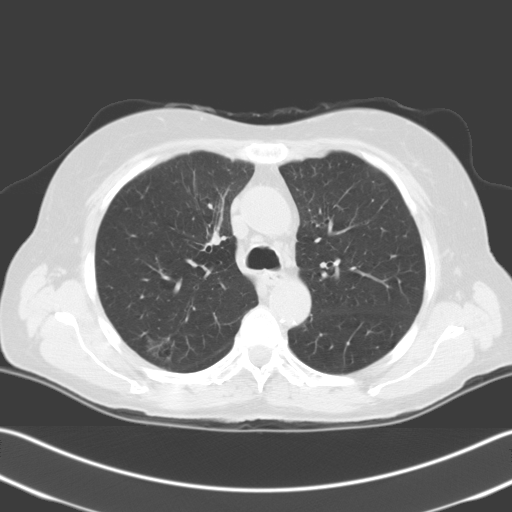
Chest CT (low-dose screening protocol), one axial image. First (baseline) screen. Lung window (W 1500 / L -600 HU). Standard (soft-tissue) reconstruction kernel (C). Female, age 67 years at enrolment. Current smoker at enrolment.
• Expert reader's lesion annotation, box from (x=124, y=326) to (x=183, y=374) px.
• The screening reader recorded 2 non-calcified nodules or masses ≥4 mm on this exam (right upper lobe, right upper lobe); which of them this box marks is not recorded.
• Official screen result: positive, change unspecified: nodule(s) >= 4 mm or enlarging nodule(s), mass(es), or other non-specific abnormalities suspicious for lung cancer.
• Participant outcome: lung cancer diagnosed 24 days after this screen — squamous cell carcinoma, NOS, right upper lobe, stage IIIA (AJCC 6th edition), 56 mm at pathology.